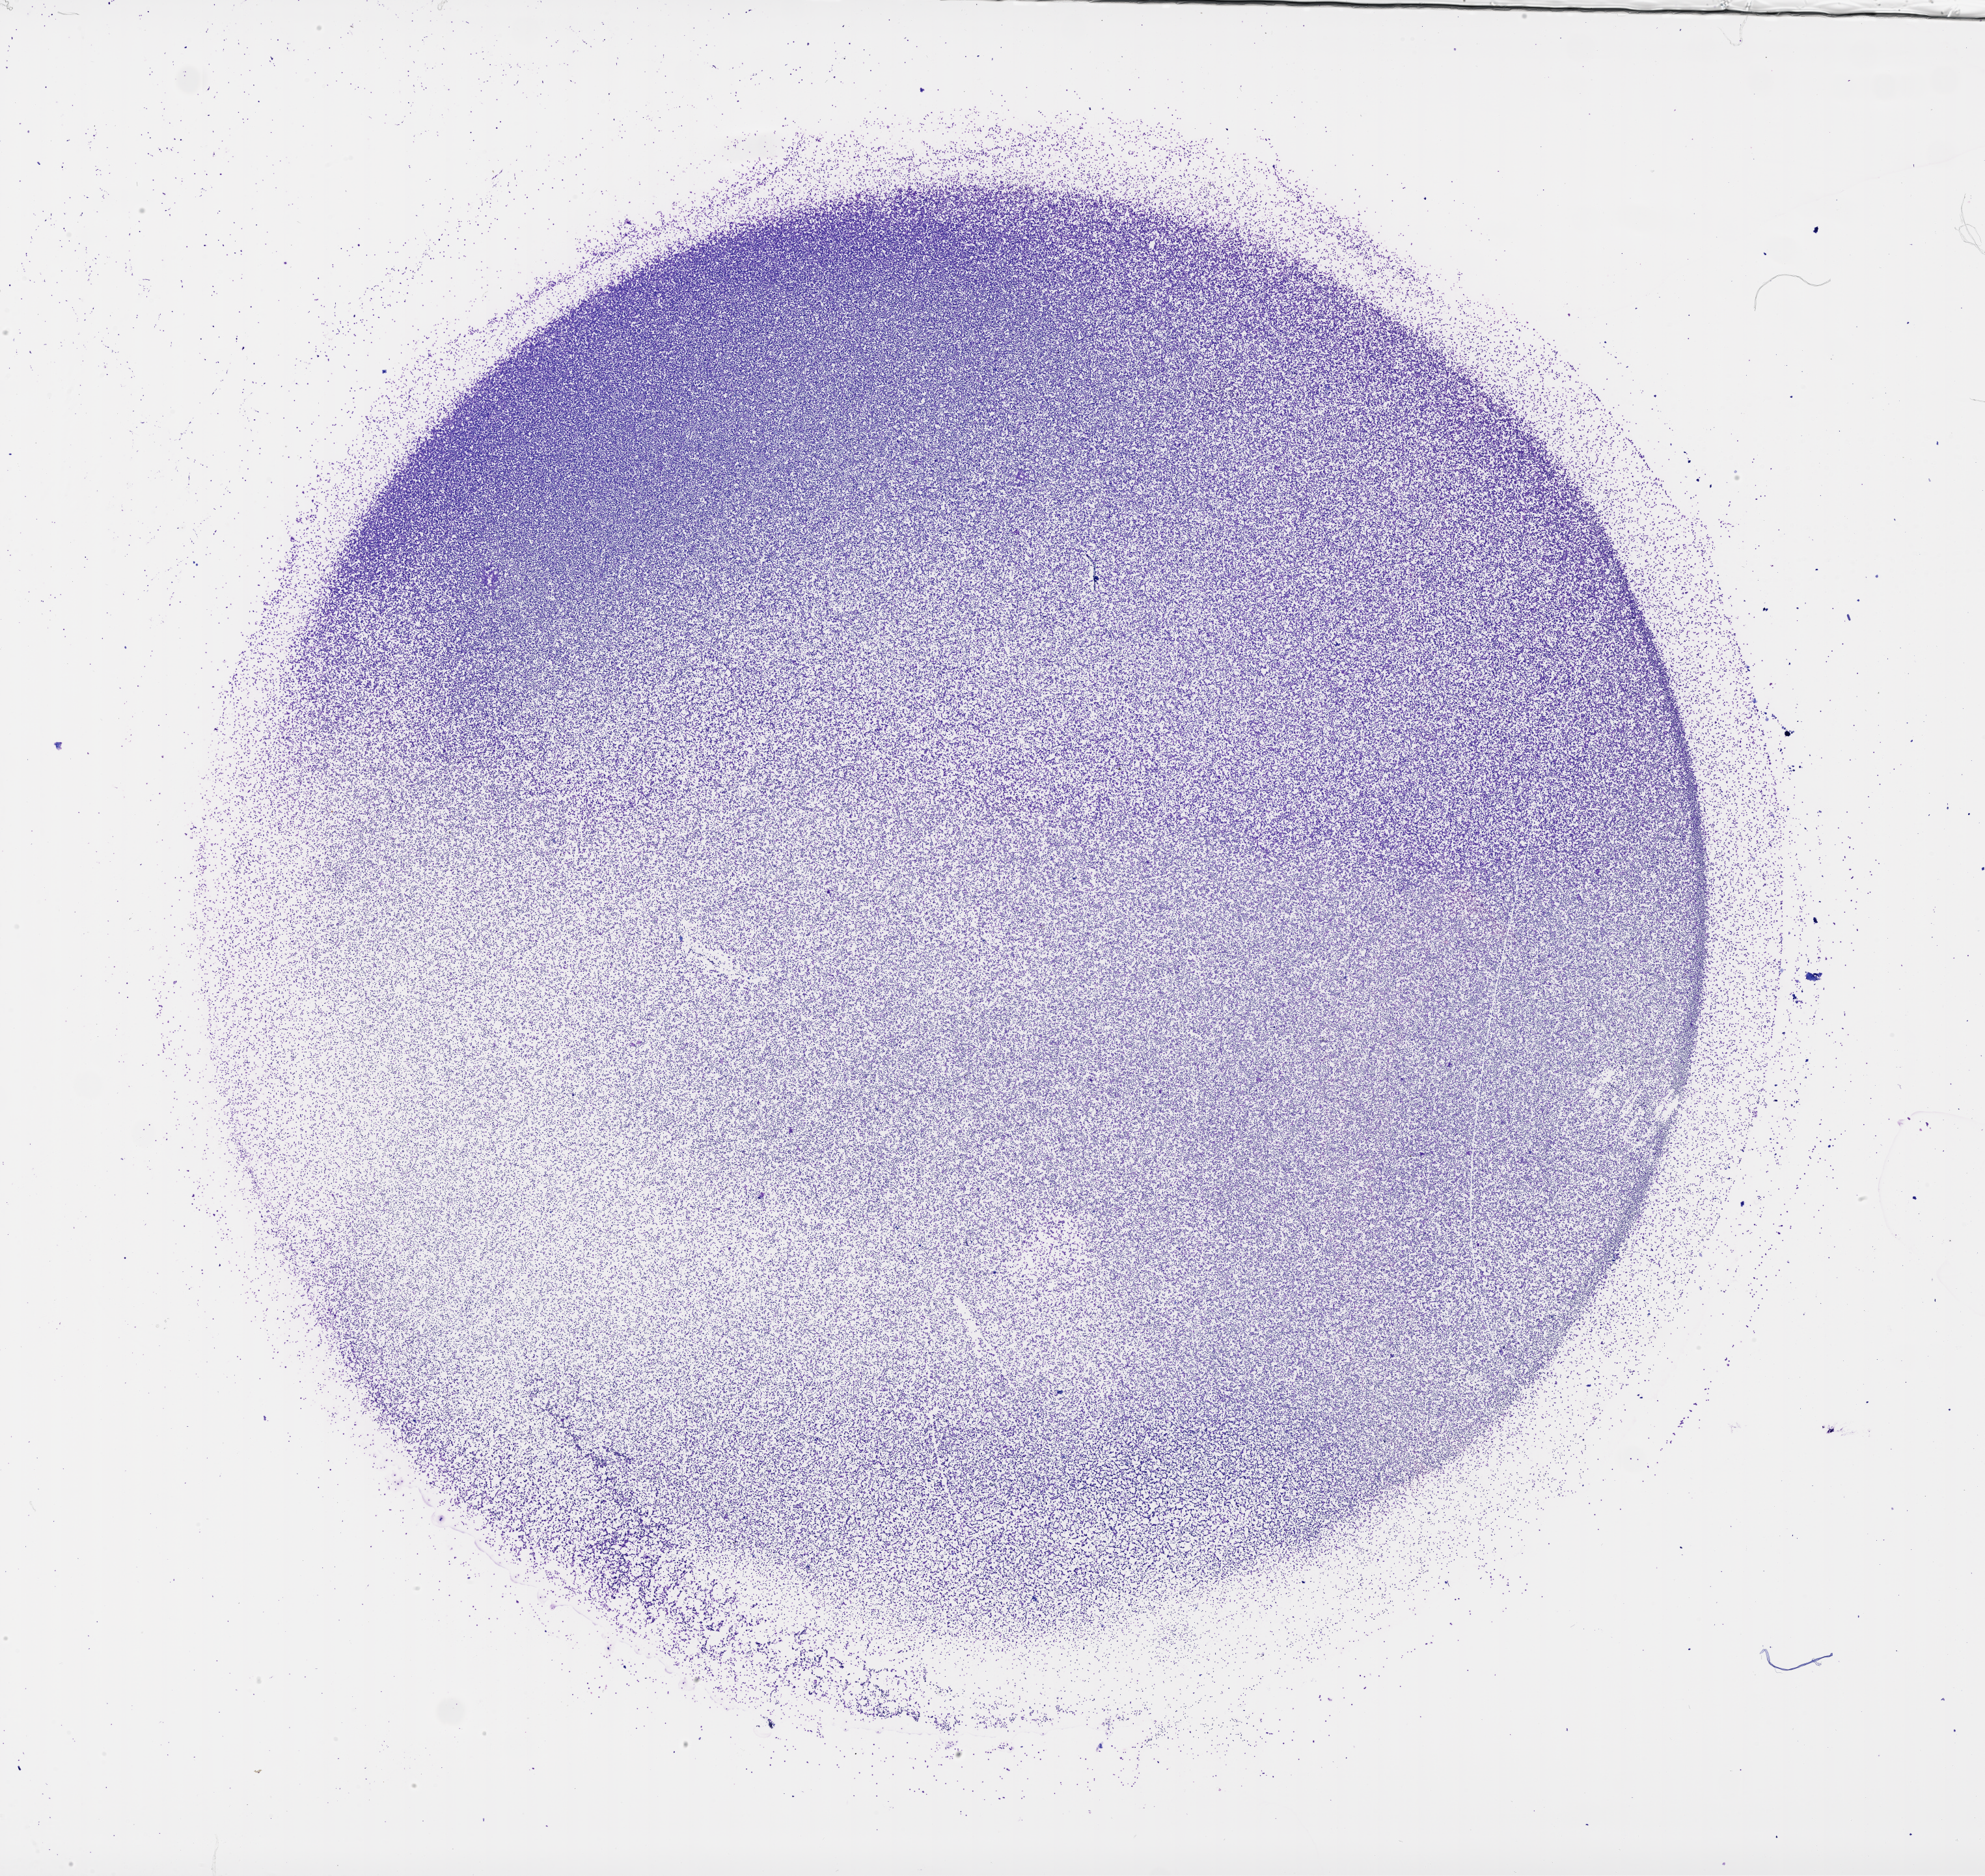
Whole-slide histology image, H&E-stained — low-resolution overview of the scanned area, about 24.6 x 23.3 mm; bone marrow (leukaemic) sample. 87-year-old female patient. Blasts: 70%.
* WHO classification: AML with maturation
* diagnosis: Acute Myeloid Leukemia
* FAB classification: M2